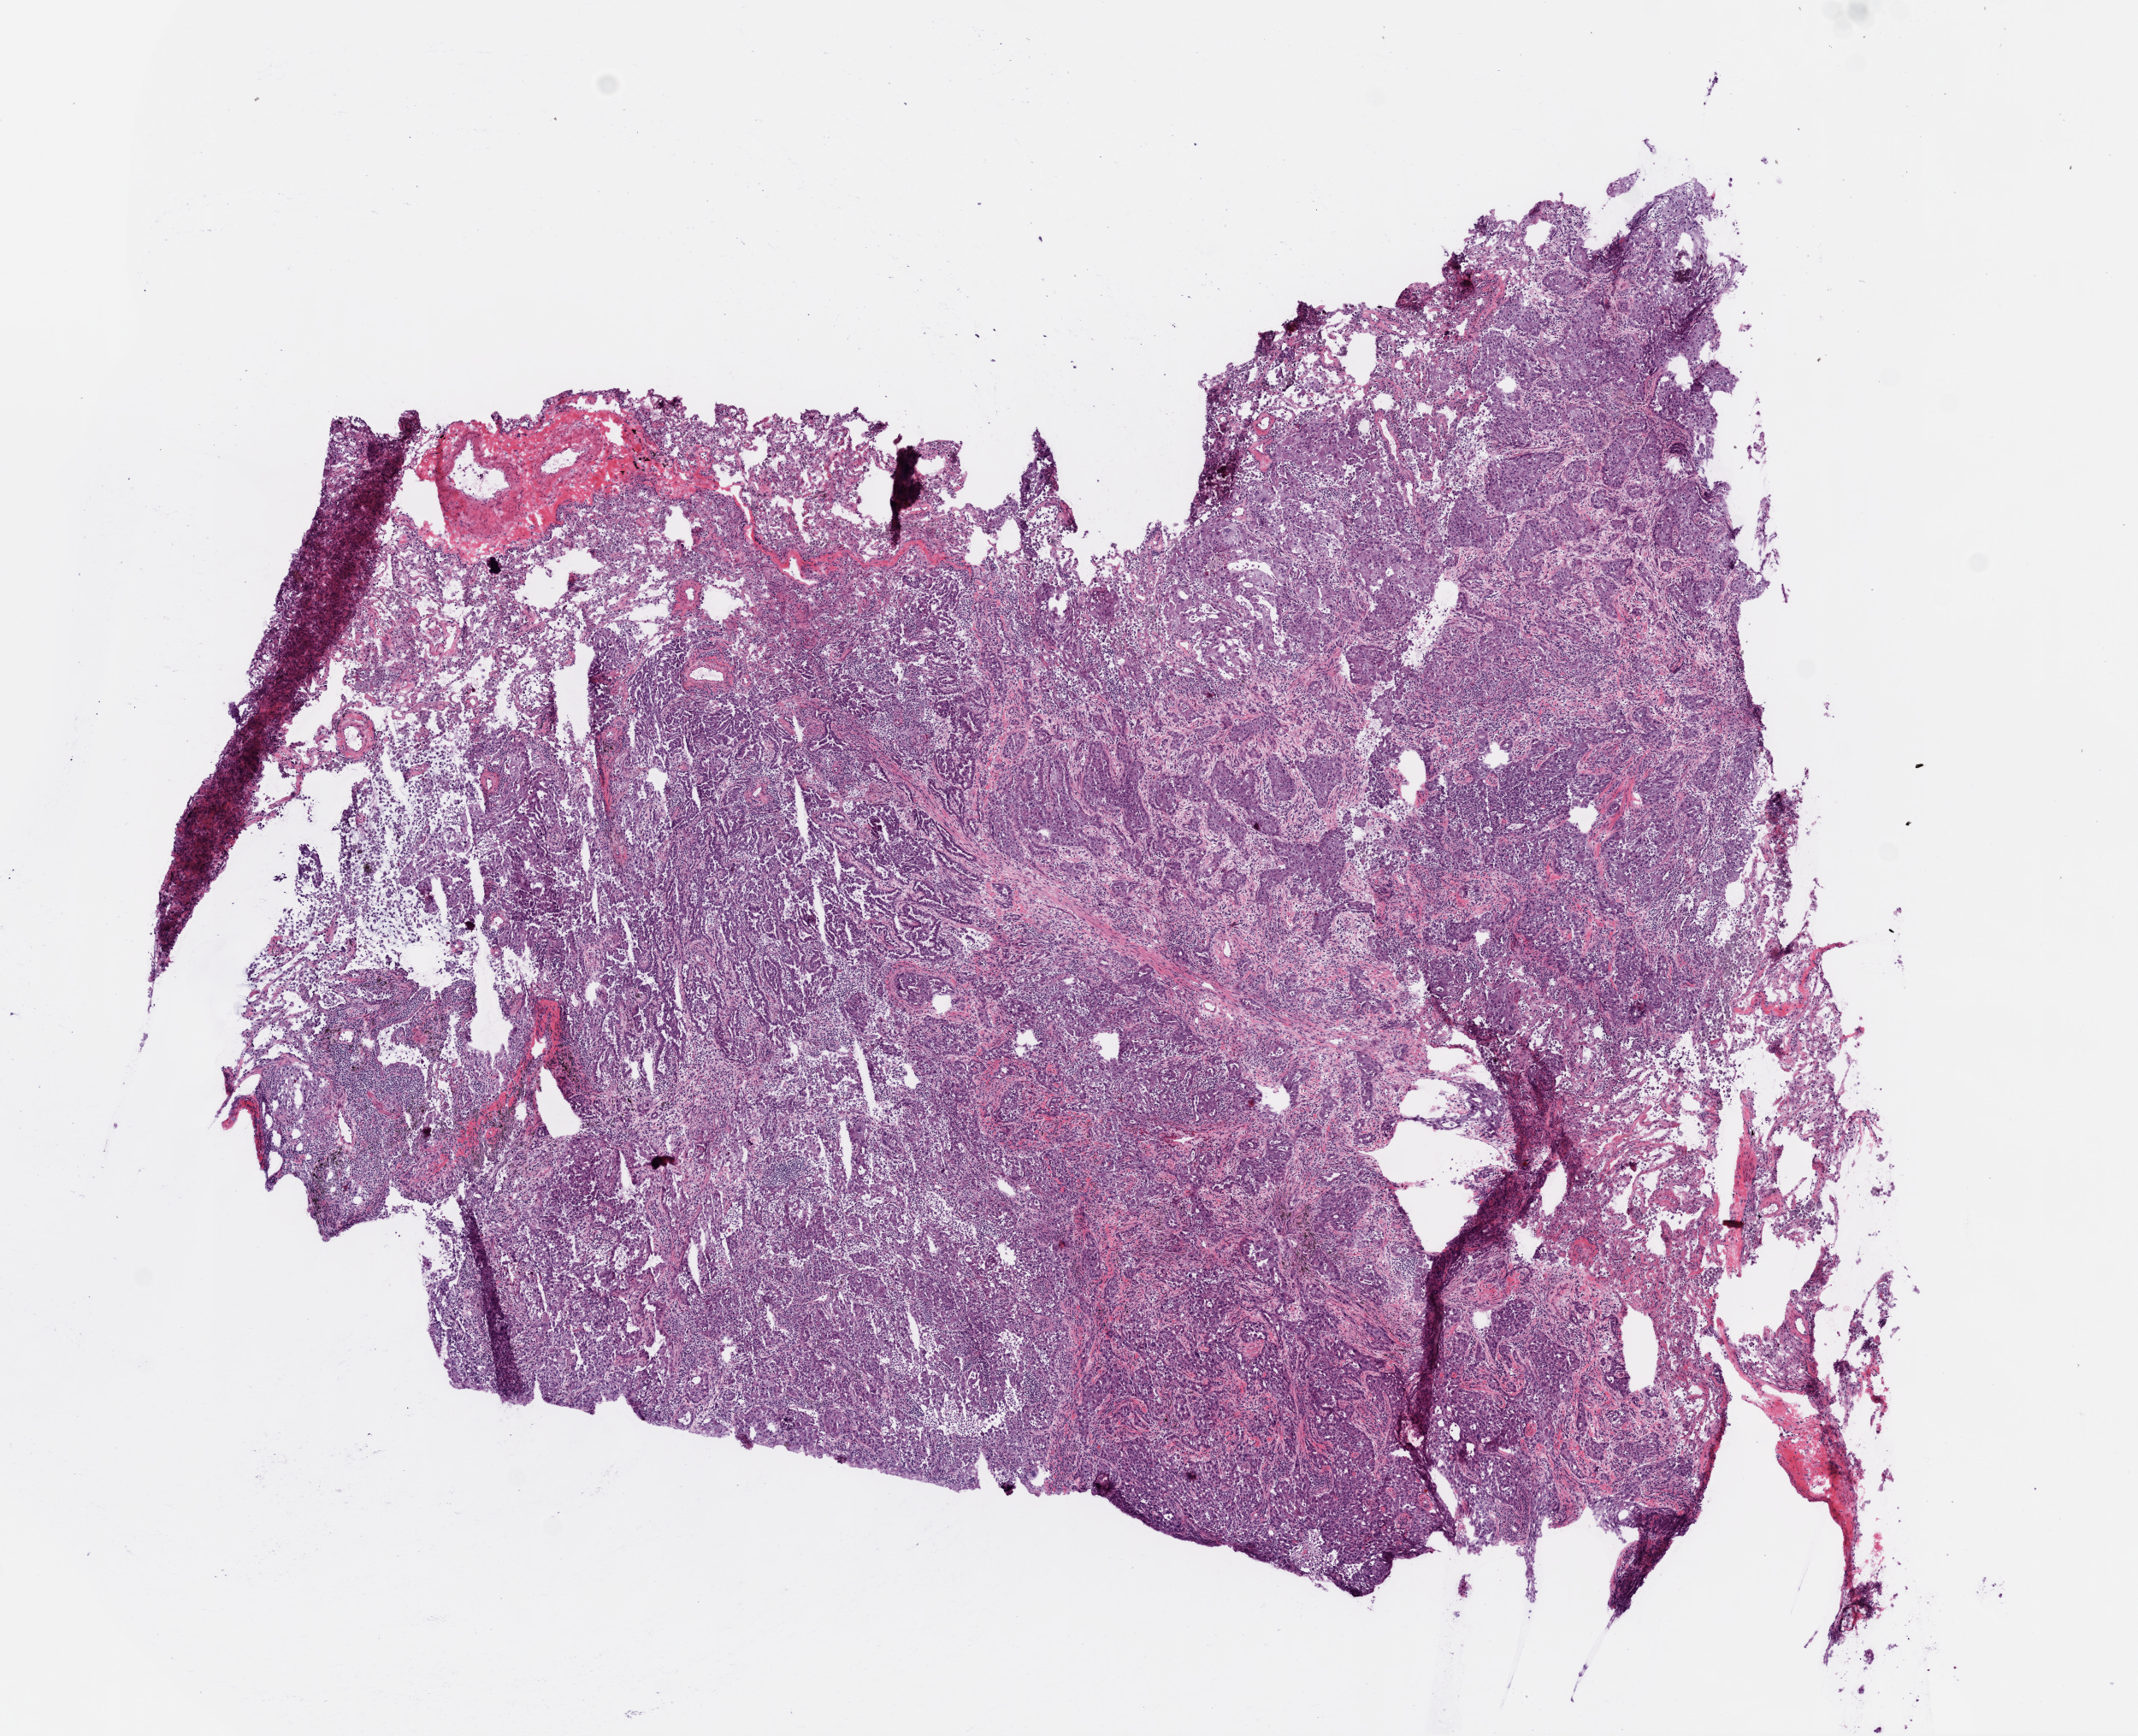
Whole-slide histology image, Hematoxylin and eosin (H&E) stained, low-resolution overview of the scanned area, about 10.0 x 8.1 mm (slide scanned at 20x). Frozen section. Lung, primary tumour sample. Male, age 59 years at initial diagnosis. Pathologist review of this section (percent, as recorded): tumour cells 85%, tumour nuclei 80%, normal cells 5%, stromal cells 10%, necrosis 0%. Infiltration values recorded for this section: lymphocyte infiltration 10%.
* TNM: T2 N0 M0
* laterality: right
* AJCC pathologic stage: IB (6th edition)
* diagnosis: Adenocarcinoma, NOS (upper lobe, lung)